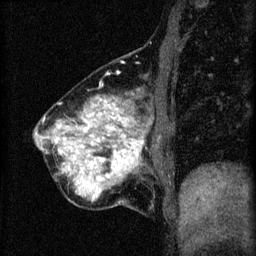
Breast MRI (dynamic contrast-enhanced), one sagittal slice; position 18 of 60 along the scan axis; 3 images stored at this slice position (order not interpretable as contrast timing); 1.5 T; TE 4.2 ms, TR 8.2 ms; 2 mm slice thickness; 256 × 256 image matrix. Female patient, age 40 years.
Outlined on this slice (semi-automatically segmented with operator editing):
- analysis volume of interest (the breast-tissue region the enhancement analysis was run in; not a lesion): bounding box (x1, y1, x2, y2) in pixels: (36, 78, 171, 211)
- tumour enhancement mask (voxels above the 70 % enhancement threshold inside the analysis volume of interest): (44, 98, 145, 199)